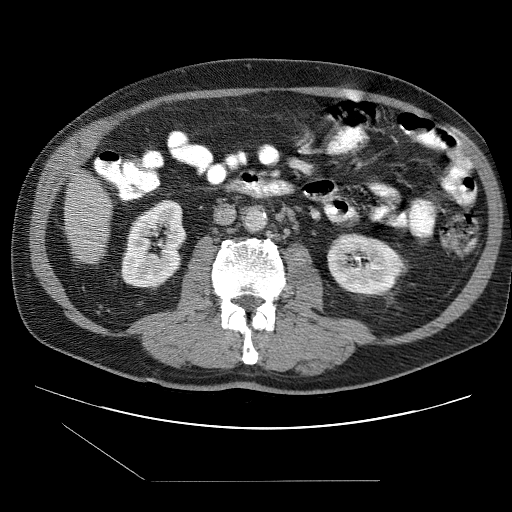
Contrast-enhanced abdominal CT (liver protocol), one axial slice; position 15 of 109 along the scan axis; reconstruction kernel STANDARD; 120 kVp; one of 2 acquisitions stored at this slice position; soft-tissue window (W 400 / L 40 HU); 2.5 mm slice thickness; 512 × 512 image matrix, field of view 400 × 400 mm. Case-level facts recorded for this patient, not image findings: diagnosis: hepatocellular carcinoma (patient treated with transarterial chemoembolisation; whether this scan precedes or follows treatment is not stated here); TNM stage (as recorded): Stage-IIIB; Child-Pugh class: A.
Structures marked on this image (semi-automatically segmented with operator editing):
- liver parenchyma outside the tumour (the mass and vessels are separate outlines, so this box may not span the whole liver): bounding box <64,176,112,262> (left, top, right, bottom; pixels)